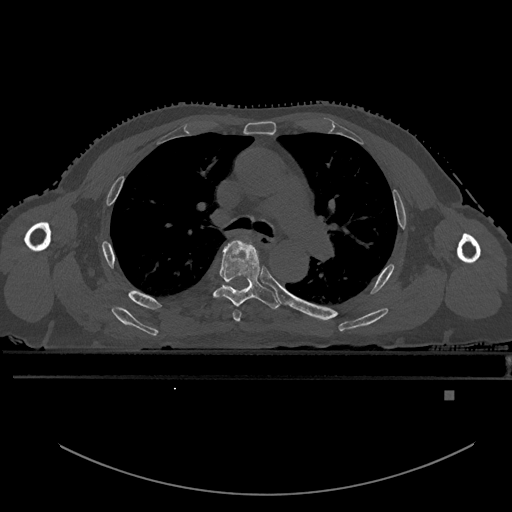
CT including the spine, one axial slice. Position 364 of 969 along the scan axis. Bone window (W 1800 / L 400 HU). 0.5 mm slice thickness. 512 × 512 image matrix, field of view 456 × 456 mm. Patient: male, 82 years. From the clinical record (not read from this slice): primary cancer: prostate; vertebrae with lytic lesions (as recorded): T11, T9, T8, T2.
Outlined on this slice (semi-automatically segmented with operator editing):
- T4 vertebra: bounding box [x1, y1, x2, y2] px = [233, 310, 241, 322]
- T5 vertebra: [213, 240, 280, 309]